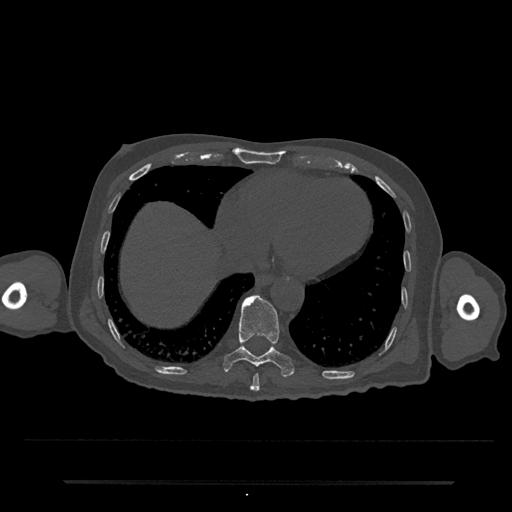
CT including the spine, one axial slice; slice 317 of 797 in the series (ordered by position); reconstruction kernel Br40s/3; bone window (W 1800 / L 400 HU); 0.5 mm slice thickness; 512 × 512 image matrix. Patient: male, 74 years. Case-level facts recorded for this patient, not image findings: primary cancer: prostate.
Outlined on this slice (semi-automatically segmented with operator editing):
- T10 vertebra: bounding box [x1, y1, x2, y2] px = [223, 295, 294, 377]
- T9 vertebra: [250, 374, 260, 392]